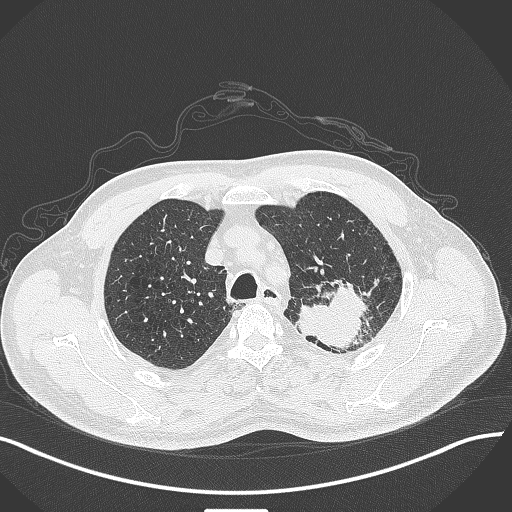
Chest CT, one axial slice. Slice 334 of 429 in the series (ordered by position). 120 kVp. Lung window (W 1500 / L -600 HU). 1 mm slice thickness. 512 × 512 image matrix, field of view 400 × 400 mm. Male patient, age 55 years. Case-level facts recorded for this patient, not image findings: clinical TNM (as recorded): T3 N0 M1c.
Annotated regions visible in this slice (rectangle marked by the reading radiologist):
- lung tumour (recorded histology: adenocarcinoma): bounding box (x1, y1, x2, y2) in pixels: (295, 278, 369, 353)